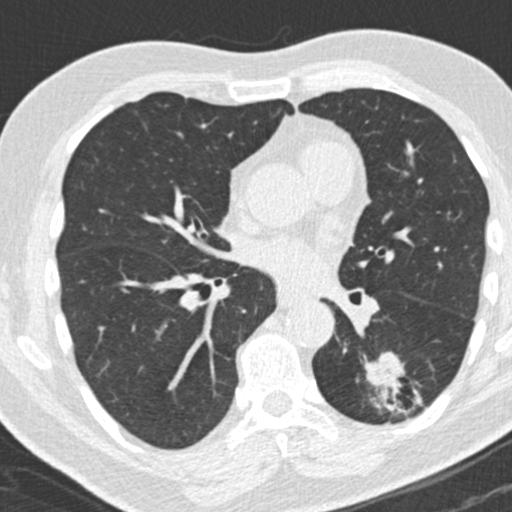
Low-dose screening chest CT, one axial slice. Position 98 of 180 along the scan axis. Reconstruction kernel B30f. 120 kVp. Lung window (W 1500 / L -600 HU). 512 × 512 image matrix, field of view 300 × 300 mm.
Structures marked on this image (manually delineated by an expert):
- lesion 1 (tumor, lower lobe of left lung): bounding box <366,352,404,388> (left, top, right, bottom; pixels)